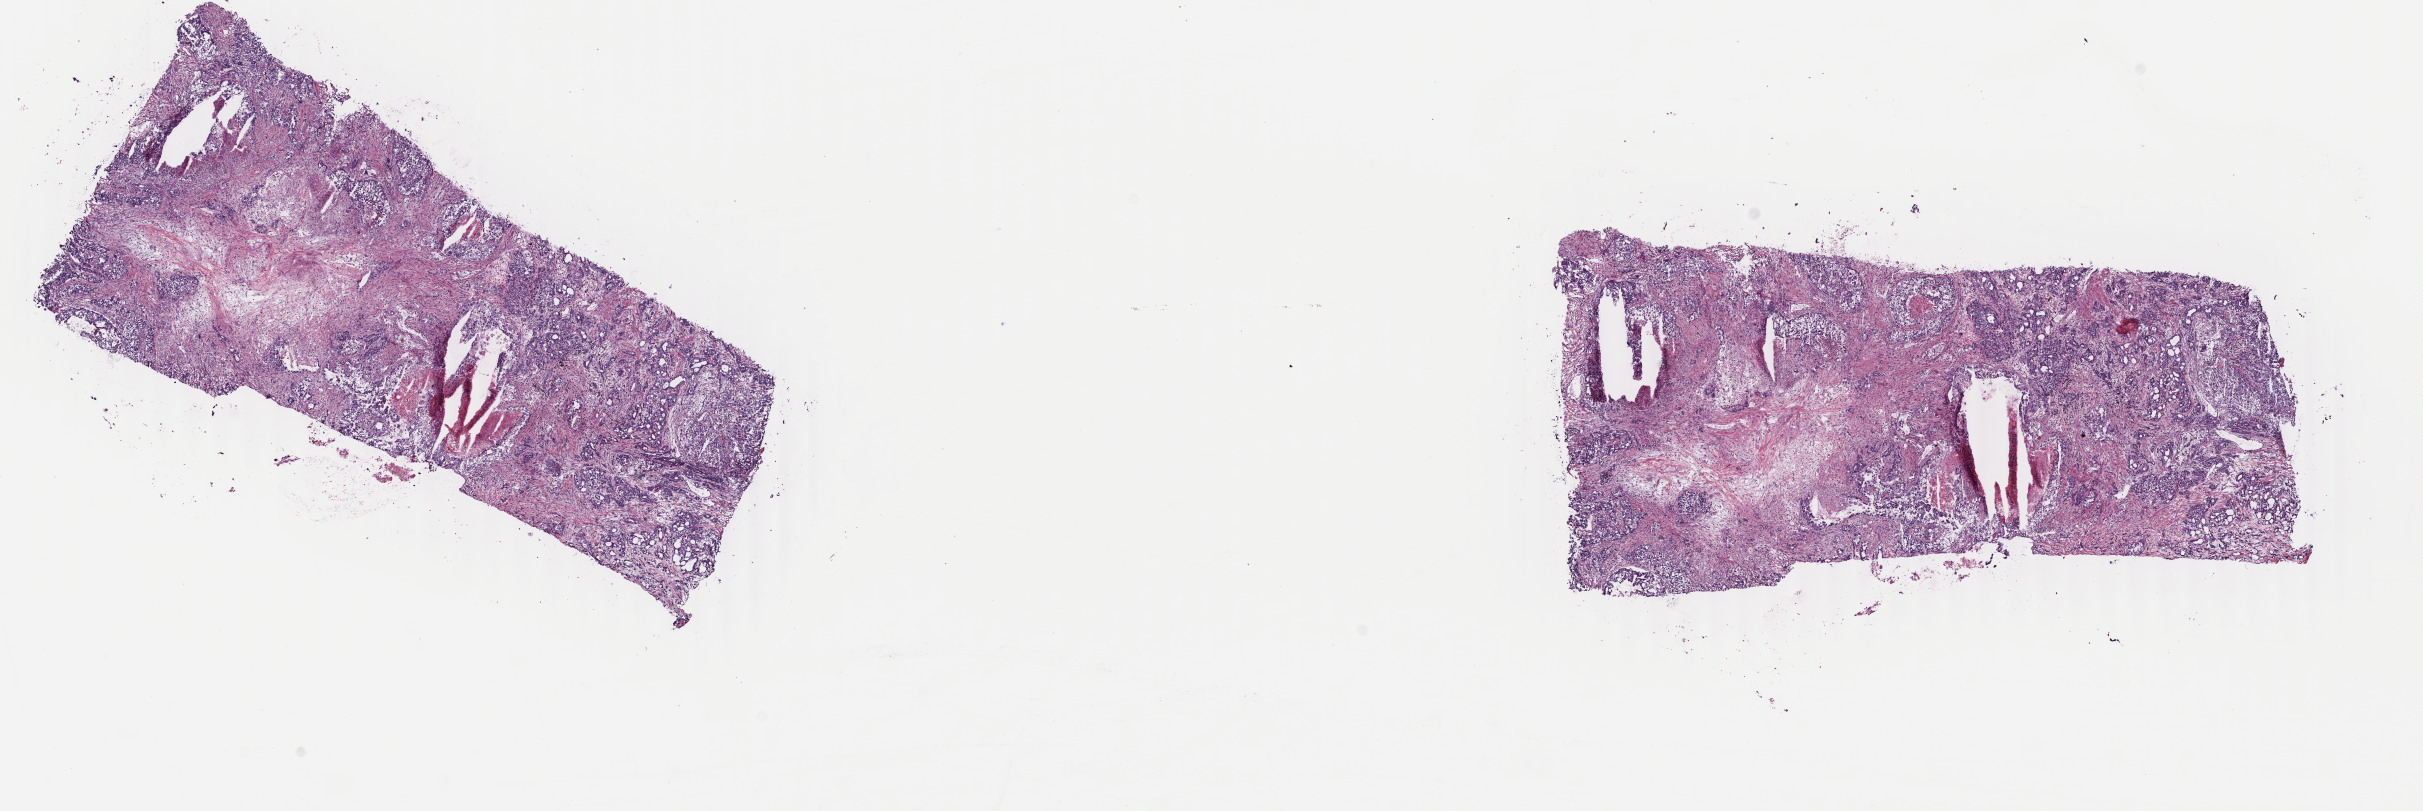
Digitized H&E tissue section (whole slide) — whole scanned area (about 19.3 x 6.5 mm, acquisition: 40x scan) shown as a low-resolution overview, frozen section, primary tumour sample from the lung. Male, age 68 years at initial diagnosis.
Histologic diagnosis: Adenocarcinoma, NOS.